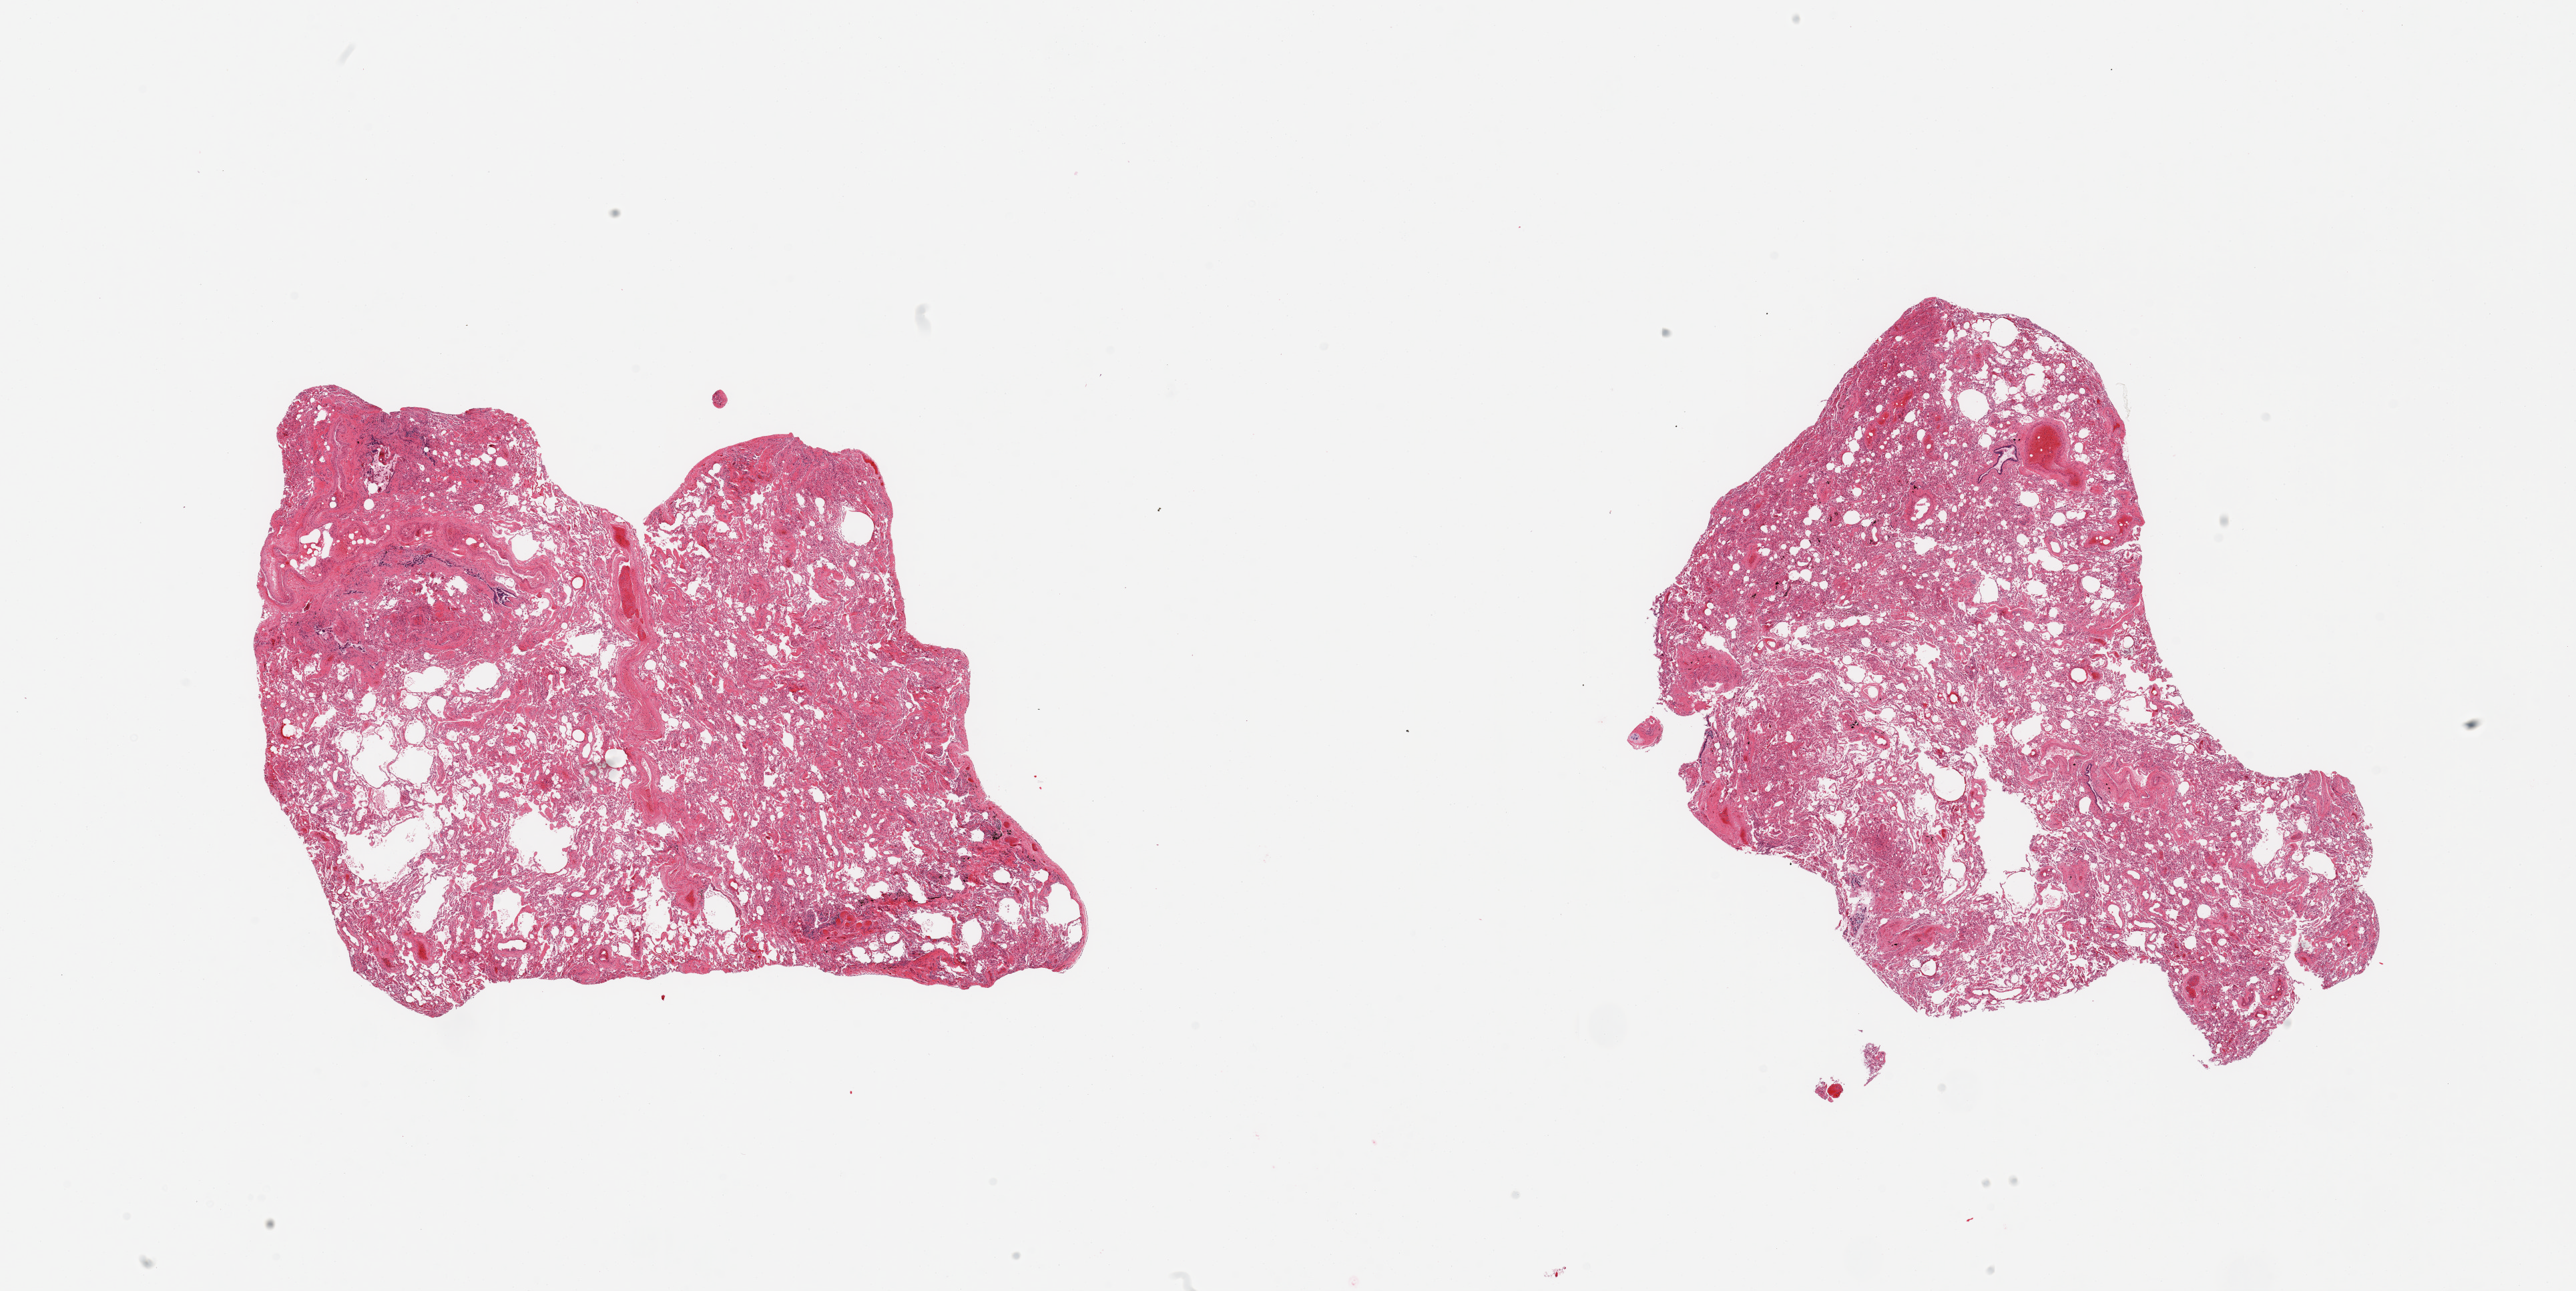
Digitized haematoxylin and eosin-stained section, brightfield, whole scanned area (about 30.5 x 15.3 mm) shown as a low-resolution overview; PAXgene-fixed paraffin-embedded (PFPE) section; sampled site (target tissue): lung; donor tissue sample. Donor: male.
Pathologist's review note for this sample: 2 pieces; congestion, some emphysematous change, includes few larger vessels.